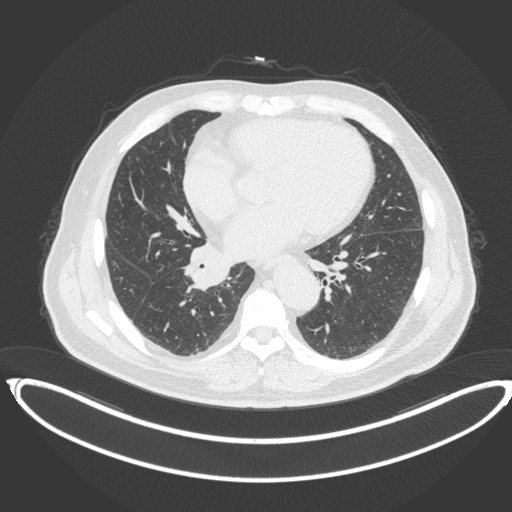
Chest CT, one axial slice. Slice 179 of 383 in the series (ordered by position). Reconstruction kernel B31f. Lung window (W 1500 / L -600 HU). 1 mm slice thickness. 512 × 512 image matrix, field of view 448 × 448 mm. Patient: male, 61 years. Case-level facts recorded for this patient, not image findings: clinical TNM (as recorded): T1b N1 M0.
Structures marked on this image (bounding box drawn by a radiologist):
- lung tumour (recorded histology: squamous cell carcinoma): bounding box <178,242,233,291> (left, top, right, bottom; pixels)